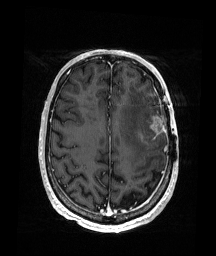
Brain MRI from a brain-tumour surgery series, one axial slice; position 63 of 176 along the scan axis; T1-weighted post-contrast; 216 × 256 image matrix. Case-level facts recorded for this patient, not image findings: histopathology: Glioblastoma; WHO grade: 4; IDH mutation: no; tumour location: Left Frontal.
Annotated regions visible in this slice (expert manual segmentation):
- tumour: bounding box <137,114,166,148> (left, top, right, bottom; pixels)